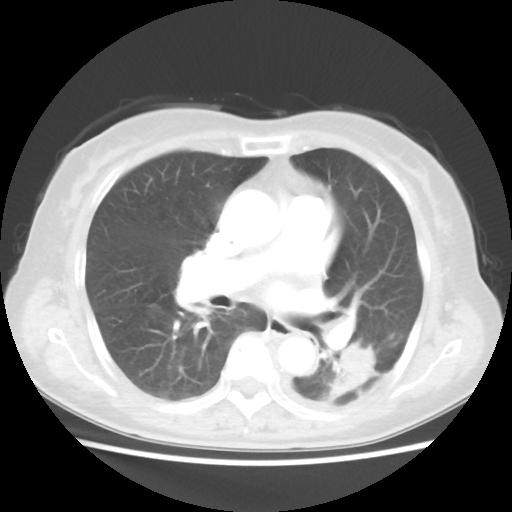
Chest CT, one axial slice; position 20 of 40 along the scan axis; 100 kVp; lung window (W 1500 / L -600 HU); 5 mm slice thickness; 512 × 512 image matrix. Patient: female, 69 years. From the clinical record (not read from this slice): clinical TNM (as recorded): T1c N0 M0.
Annotated regions visible in this slice (rectangle marked by the reading radiologist):
- lung tumour (recorded histology: adenocarcinoma): bounding box (x1, y1, x2, y2) in pixels: (328, 342, 382, 403)